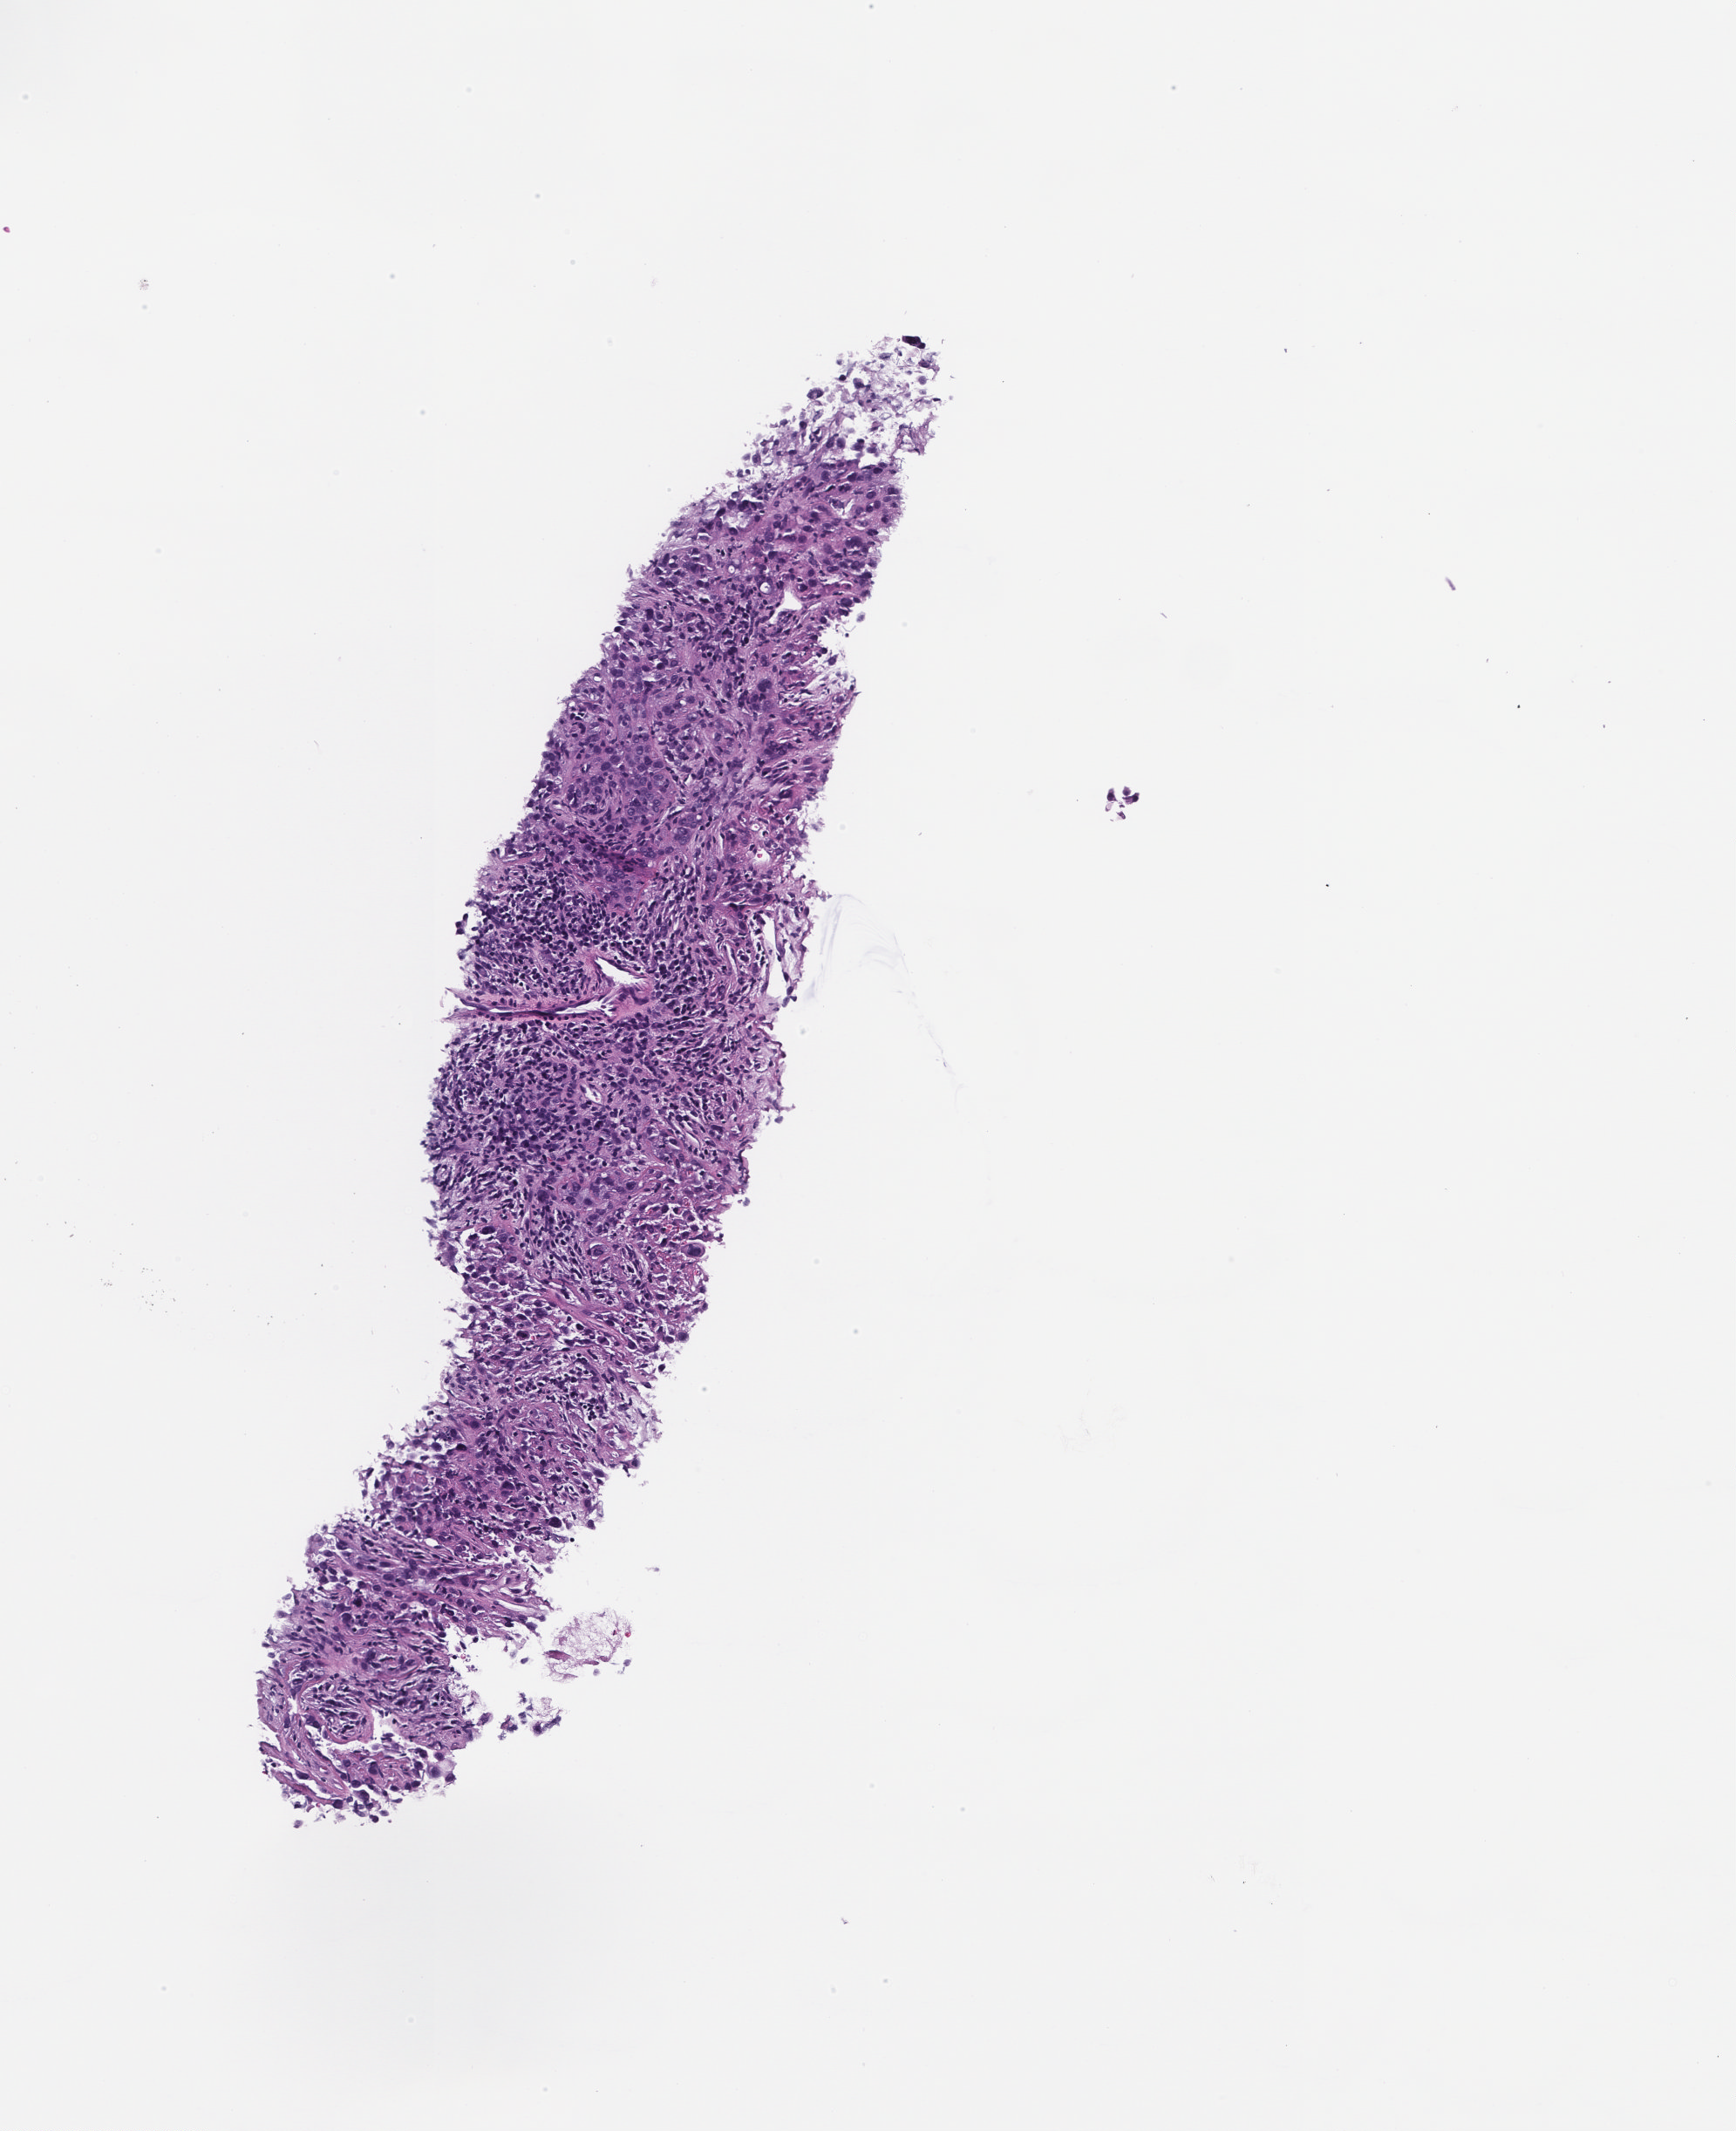
H&E whole-slide image, shown as a low-resolution overview of the whole scanned area (about 2.0 x 2.5 mm). Formalin-fixed, paraffin-embedded (FFPE) tissue. Tissue site: lung. Male patient.
This section: primary tumor. Diagnosis: Non-Small Cell Lung Carcinoma.